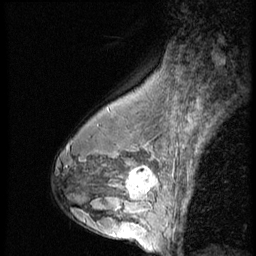
Breast MRI (dynamic contrast-enhanced), one sagittal slice; position 38 of 56 along the scan axis; 3 images stored at this slice position (order not interpretable as contrast timing); 1.5 T; TE 4.2 ms, TR 9 ms; 256 × 256 image matrix, field of view 180 × 180 mm. Female patient, age 43 years. From the clinical record (not read from this slice): setting: breast cancer imaged before/during neoadjuvant chemotherapy; receptor status: HR-positive, HER2-negative.
Outlined on this slice (semi-automatically segmented with operator editing):
- analysis volume of interest (the breast-tissue region the enhancement analysis was run in; not a lesion): bounding box [x1, y1, x2, y2] px = [120, 160, 163, 207]
- tumour enhancement mask (voxels above the 140 % enhancement threshold inside the analysis volume of interest): [127, 166, 159, 205]